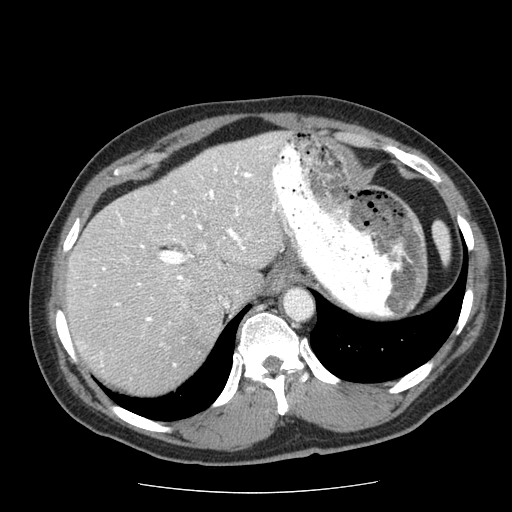
Contrast-enhanced abdominal CT (liver protocol), one axial slice; slice 46 of 85 in the series (ordered by position); reconstruction kernel STANDARD; 120 kVp; soft-tissue window (W 400 / L 40 HU); 512 × 512 image matrix. Case-level facts recorded for this patient, not image findings: diagnosis: hepatocellular carcinoma (patient treated with transarterial chemoembolisation; whether this scan precedes or follows treatment is not stated here); TNM stage (as recorded): Stage-IIIA; Child-Pugh class: A; tumour differentiation: well differentiated; tumour nodularity: multinodular.
Structures marked on this image (semi-automatically segmented with operator editing):
- liver parenchyma outside the tumour (the mass and vessels are separate outlines, so this box may not span the whole liver): bounding box [x1, y1, x2, y2] px = [66, 132, 300, 394]
- mass: [170, 292, 226, 362]
- liver vessels: [77, 144, 300, 366]